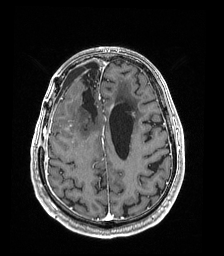
Brain MRI from a brain-tumour surgery series, one axial slice; slice 60 of 192 in the series (ordered by position); T1-weighted post-contrast; 1 mm slice thickness; 224 × 256 image matrix, field of view 224 × 256 mm. From the clinical record (not read from this slice): histopathology: Astrocytoma; WHO grade: 4.
Outlined on this slice (expert manual segmentation):
- previous resection cavity: bounding box <82,68,98,120> (left, top, right, bottom; pixels)
- tumour: <73,140,75,143>